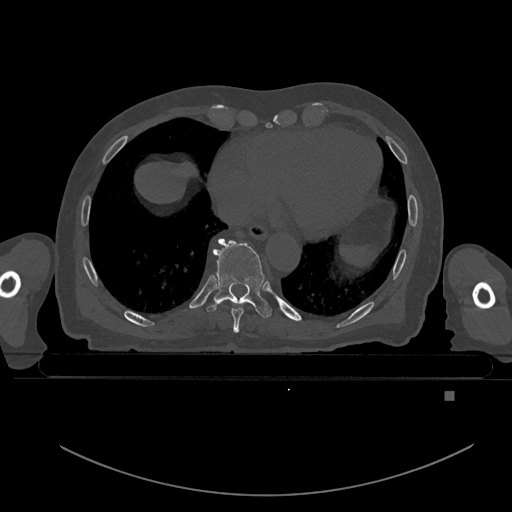
CT including the spine, one axial slice. Position 163 of 969 along the scan axis. Bone window (W 1800 / L 400 HU). 0.5 mm slice thickness. 512 × 512 image matrix. Patient: male, 82 years. Case-level facts recorded for this patient, not image findings: primary cancer: prostate; vertebrae with lytic lesions (as recorded): T11, T9, T8, T2.
Structures marked on this image (semi-automatically segmented with operator editing):
- T8 vertebra: box from (x=220, y=299) to (x=246, y=332) px
- T9 vertebra: (x=207, y=238)–(x=272, y=318)